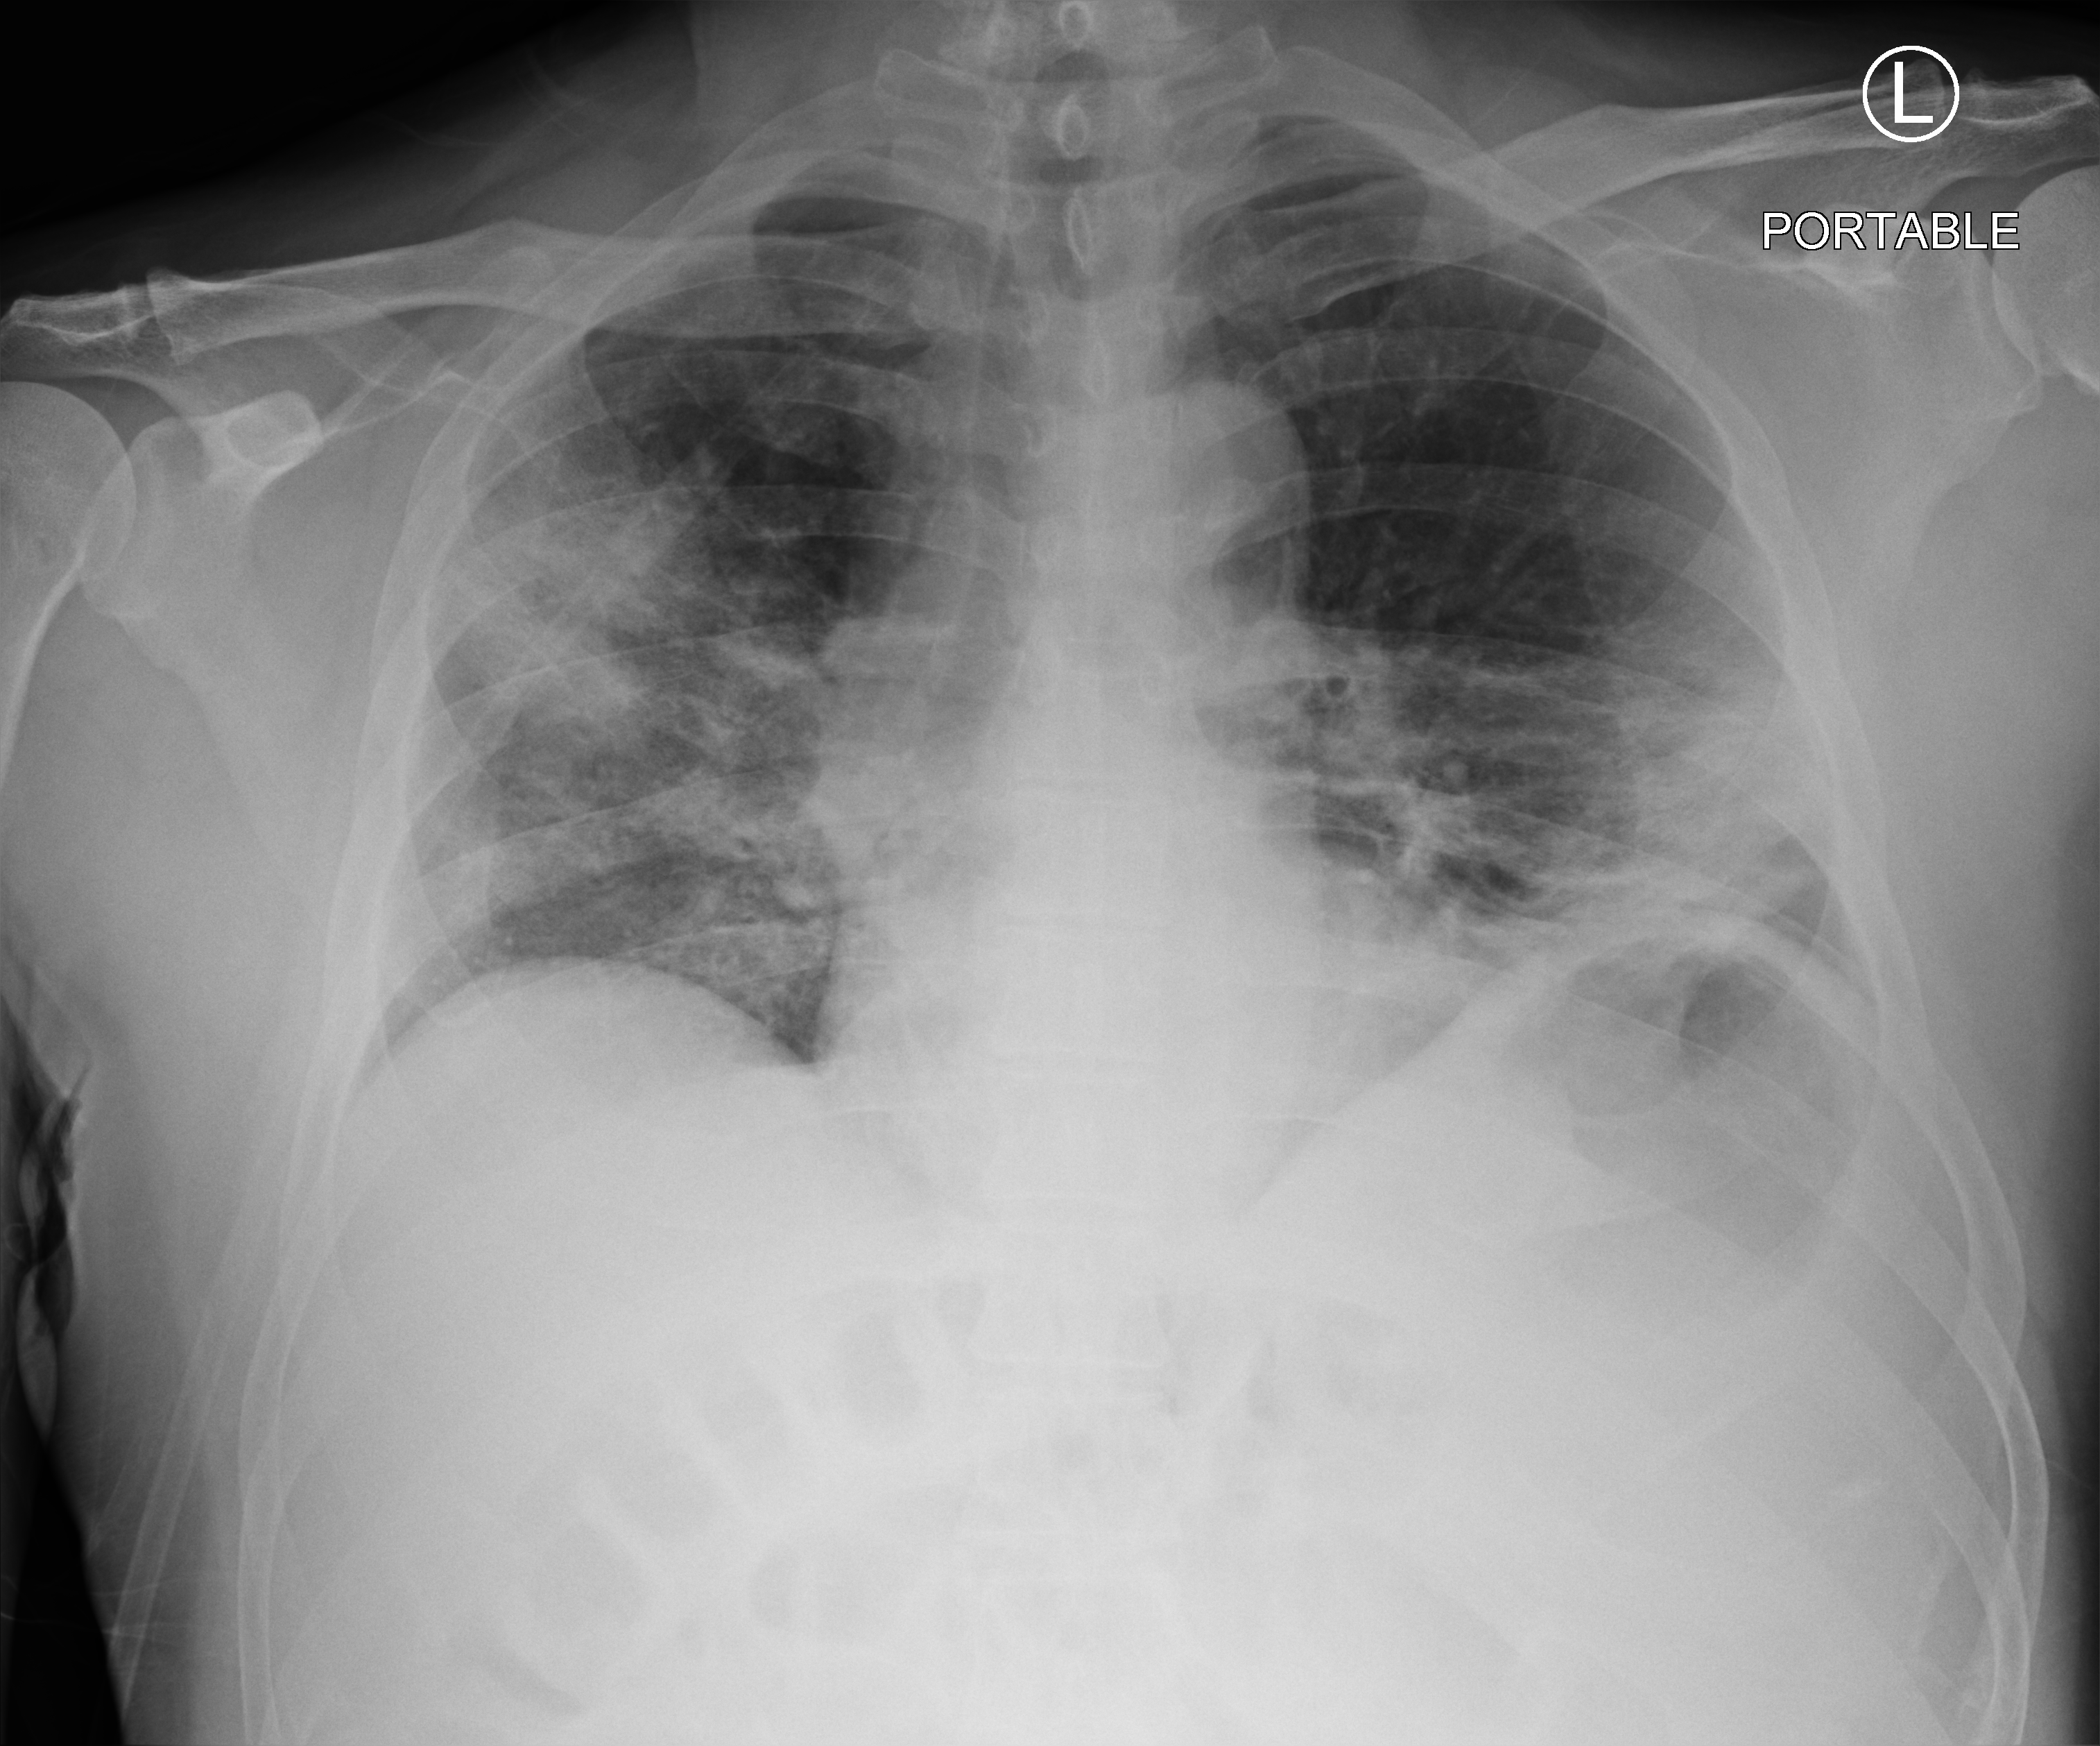
Chest X-ray (portable); anteroposterior (AP) projection. Patient hospitalised with COVID-19; male, aged 60–74 years.
From the hospital-stay record, not from the radiograph (when in the stay this image was taken is not recorded): length of hospital stay: 10 days; diabetes (admission record): no.